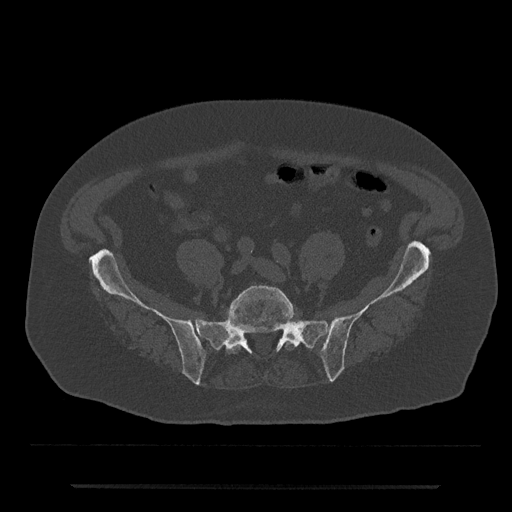
CT including the spine, one axial slice. Position 258 of 797 along the scan axis. Reconstruction kernel Br40s/3. 120 kVp. Bone window (W 1800 / L 400 HU). 512 × 512 image matrix, field of view 434 × 434 mm. Male patient, age 80 years. Case-level facts recorded for this patient, not image findings: primary cancer: prostate.
Annotated regions visible in this slice (semi-automatic segmentation, software-assisted and operator-edited):
- L5 vertebra: bounding box <226,285,296,354> (left, top, right, bottom; pixels)